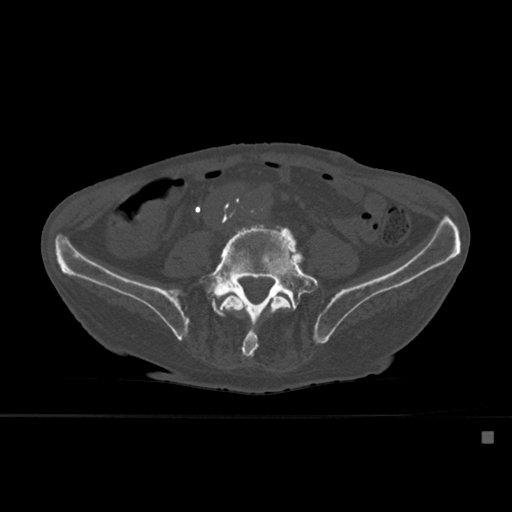
CT including the spine, one axial slice. Bone window (W 1800 / L 400 HU). 512 × 512 image matrix, field of view 373 × 373 mm. Male patient, age 78 years. From the clinical record (not read from this slice): primary cancer: prostate.
Outlined on this slice (semi-automatic segmentation, software-assisted and operator-edited):
- L4 vertebra: bounding box [x1, y1, x2, y2] px = [220, 292, 294, 359]
- L5 vertebra: [199, 227, 319, 327]